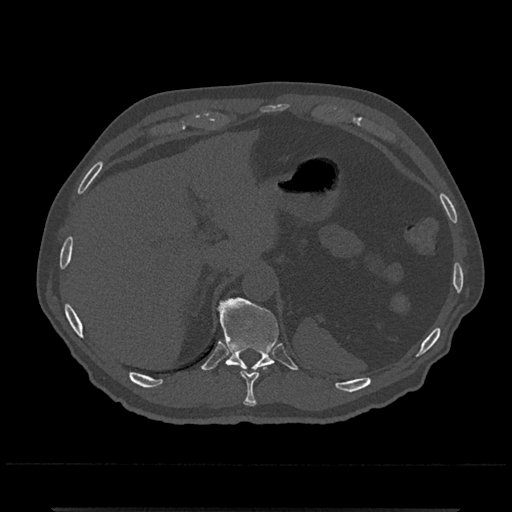
CT including the spine, one axial slice; slice 518 of 797 in the series (ordered by position); reconstruction kernel Br40s/3; 120 kVp; bone window (W 1800 / L 400 HU); 512 × 512 image matrix, field of view 393 × 393 mm. Patient: male, 67 years. Case-level facts recorded for this patient, not image findings: primary cancer: prostate.
Outlined on this slice (semi-automatic segmentation, software-assisted and operator-edited):
- T10 vertebra: bounding box (x1, y1, x2, y2) in pixels: (241, 367, 259, 407)
- T11 vertebra: (220, 298, 278, 371)